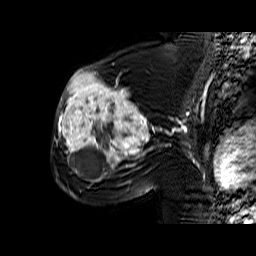
Breast MRI (dynamic contrast-enhanced), one sagittal slice; dynamic contrast-enhanced series, time point 2 of 6 at this slice position (early post-contrast); 1.5 T; TE 6.4 ms, TR 32.9 ms; 256 × 256 image matrix, field of view 200 × 200 mm. Female patient. Case-level facts recorded for this patient, not image findings: setting: breast cancer imaged before/during neoadjuvant chemotherapy; receptor status: triple-negative.
Annotated regions visible in this slice (semi-automatically segmented with operator editing):
- analysis volume of interest (the breast-tissue region the enhancement analysis was run in; not a lesion): box from (x=56, y=65) to (x=159, y=174) px
- tumour enhancement mask (voxels above the 100 % enhancement threshold inside the analysis volume of interest): (x=57, y=68)–(x=153, y=173)